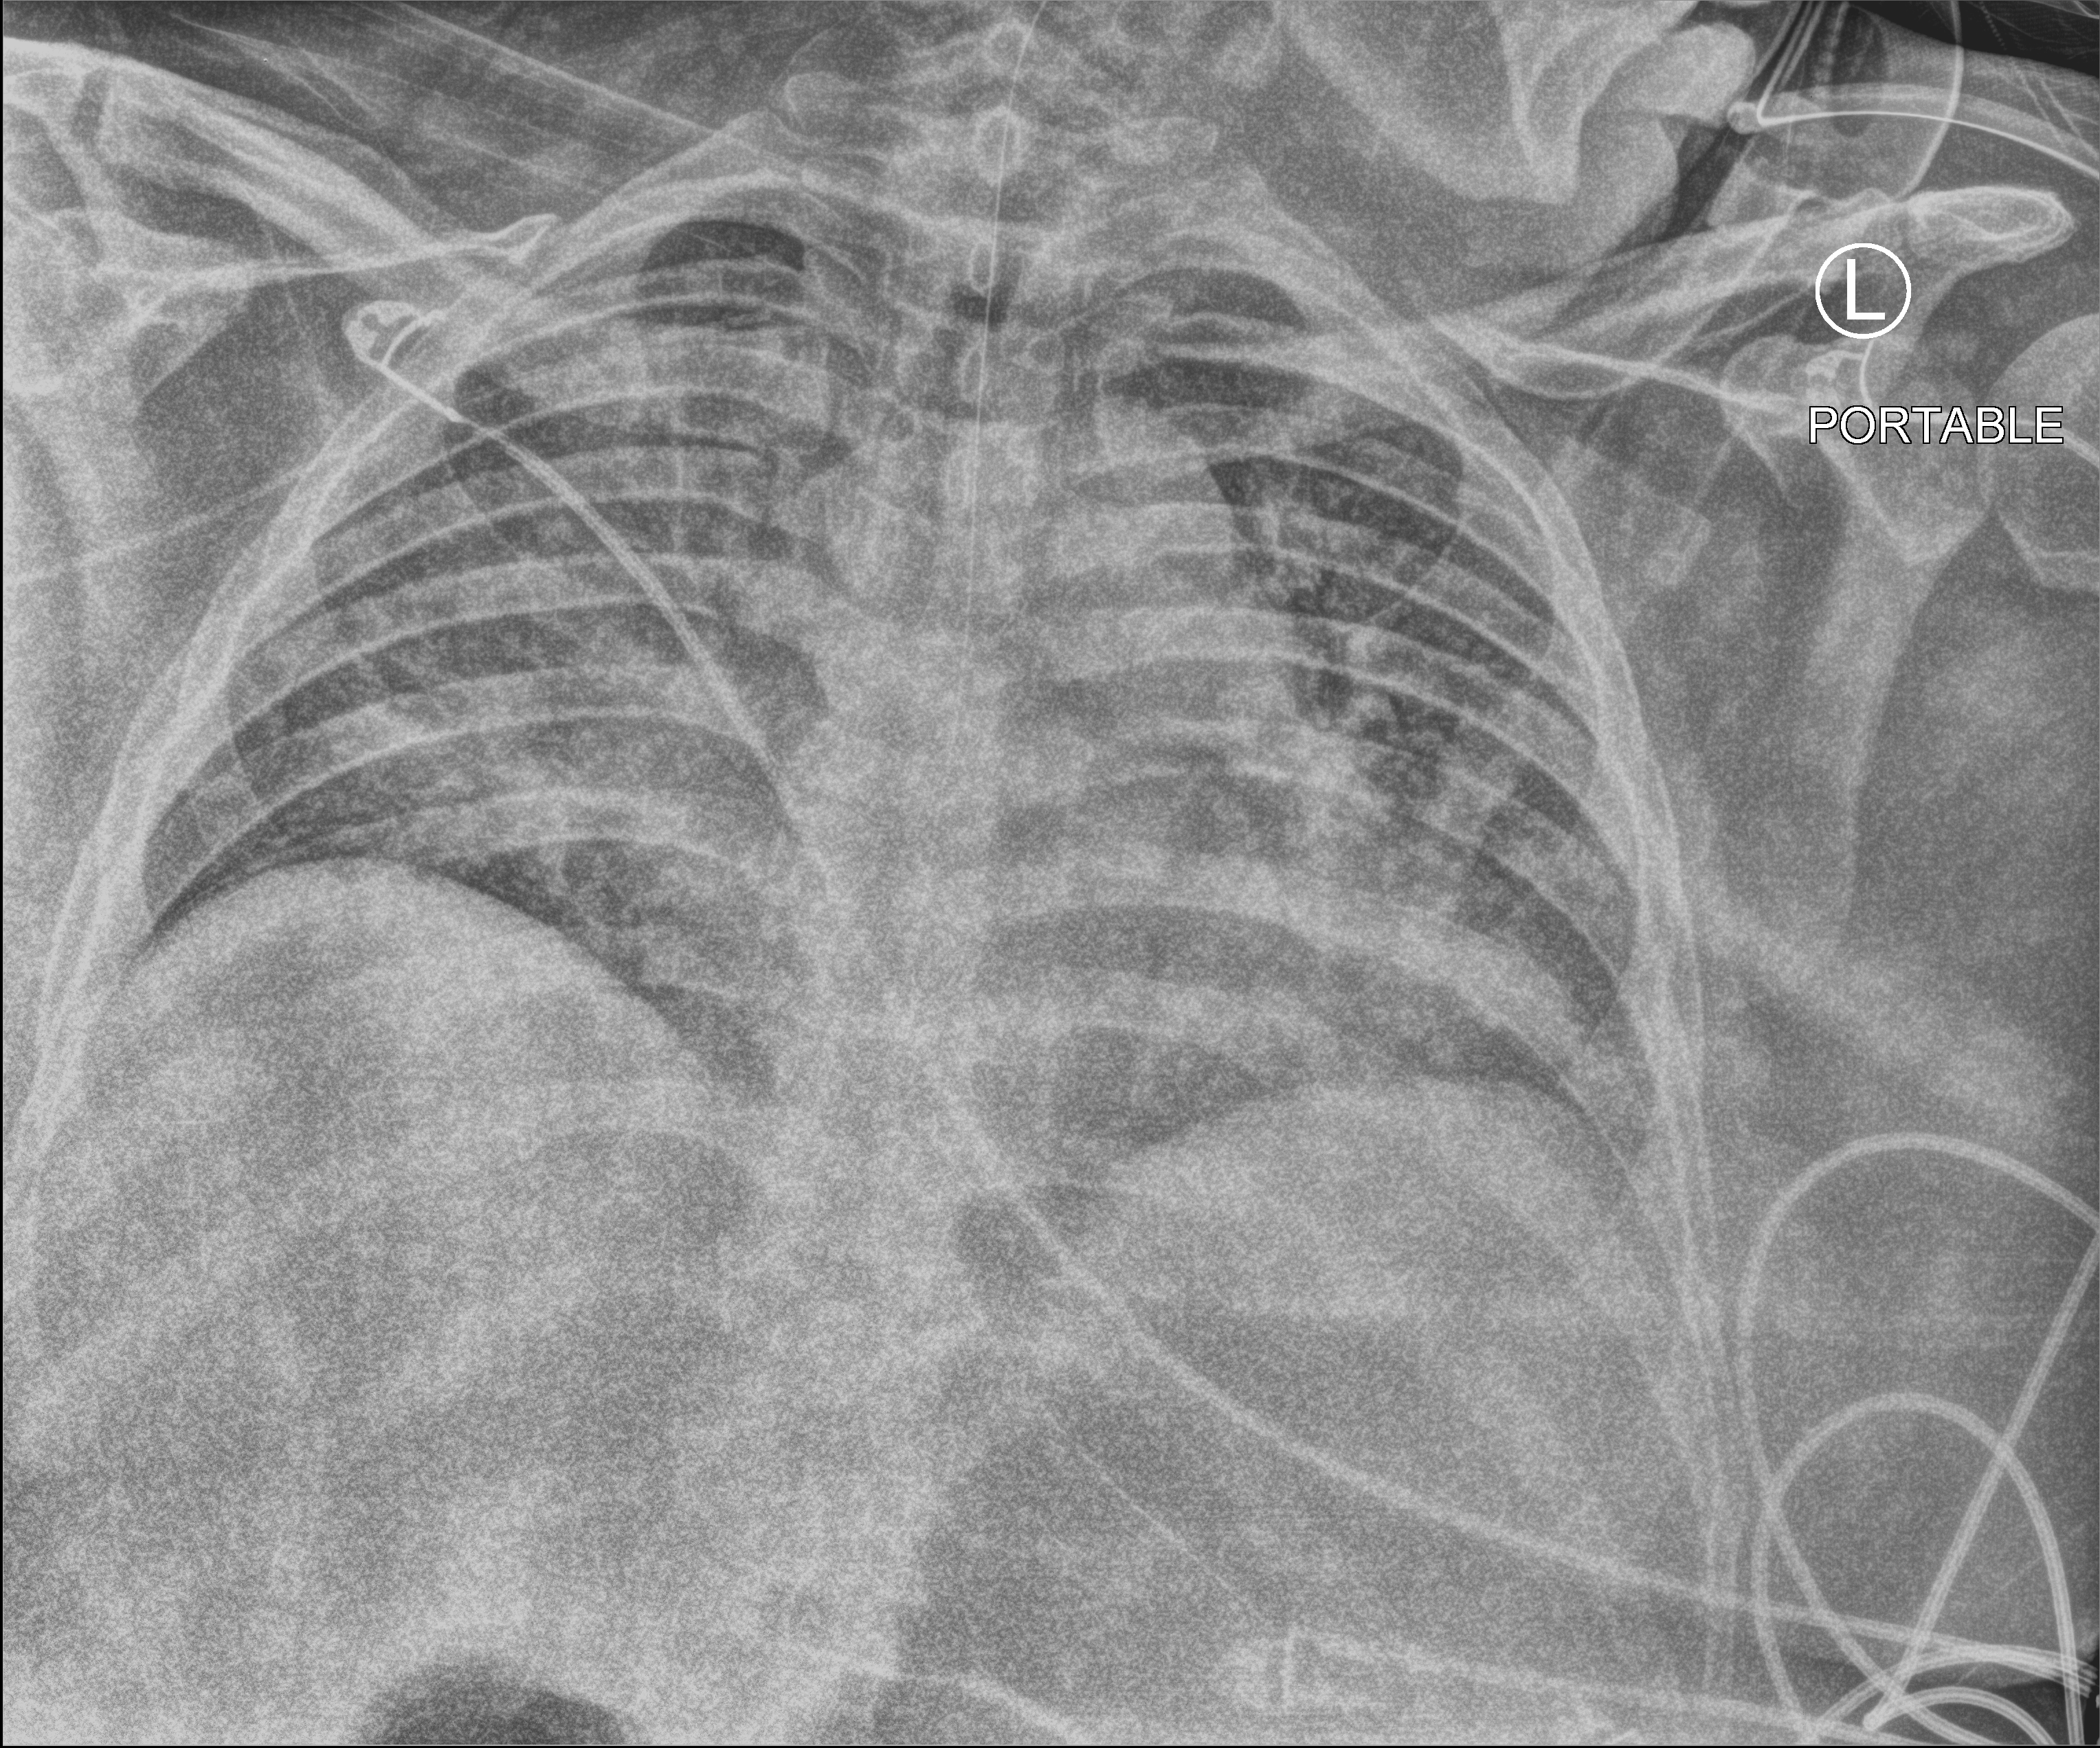
Bedside chest radiograph (computed radiography); anteroposterior (AP) projection. Patient hospitalised with COVID-19; male, aged 18–59 years.
Admission-level facts for this patient (not findings on this image; timing relative to this image not recorded): mechanically ventilated during this hospital stay: yes.